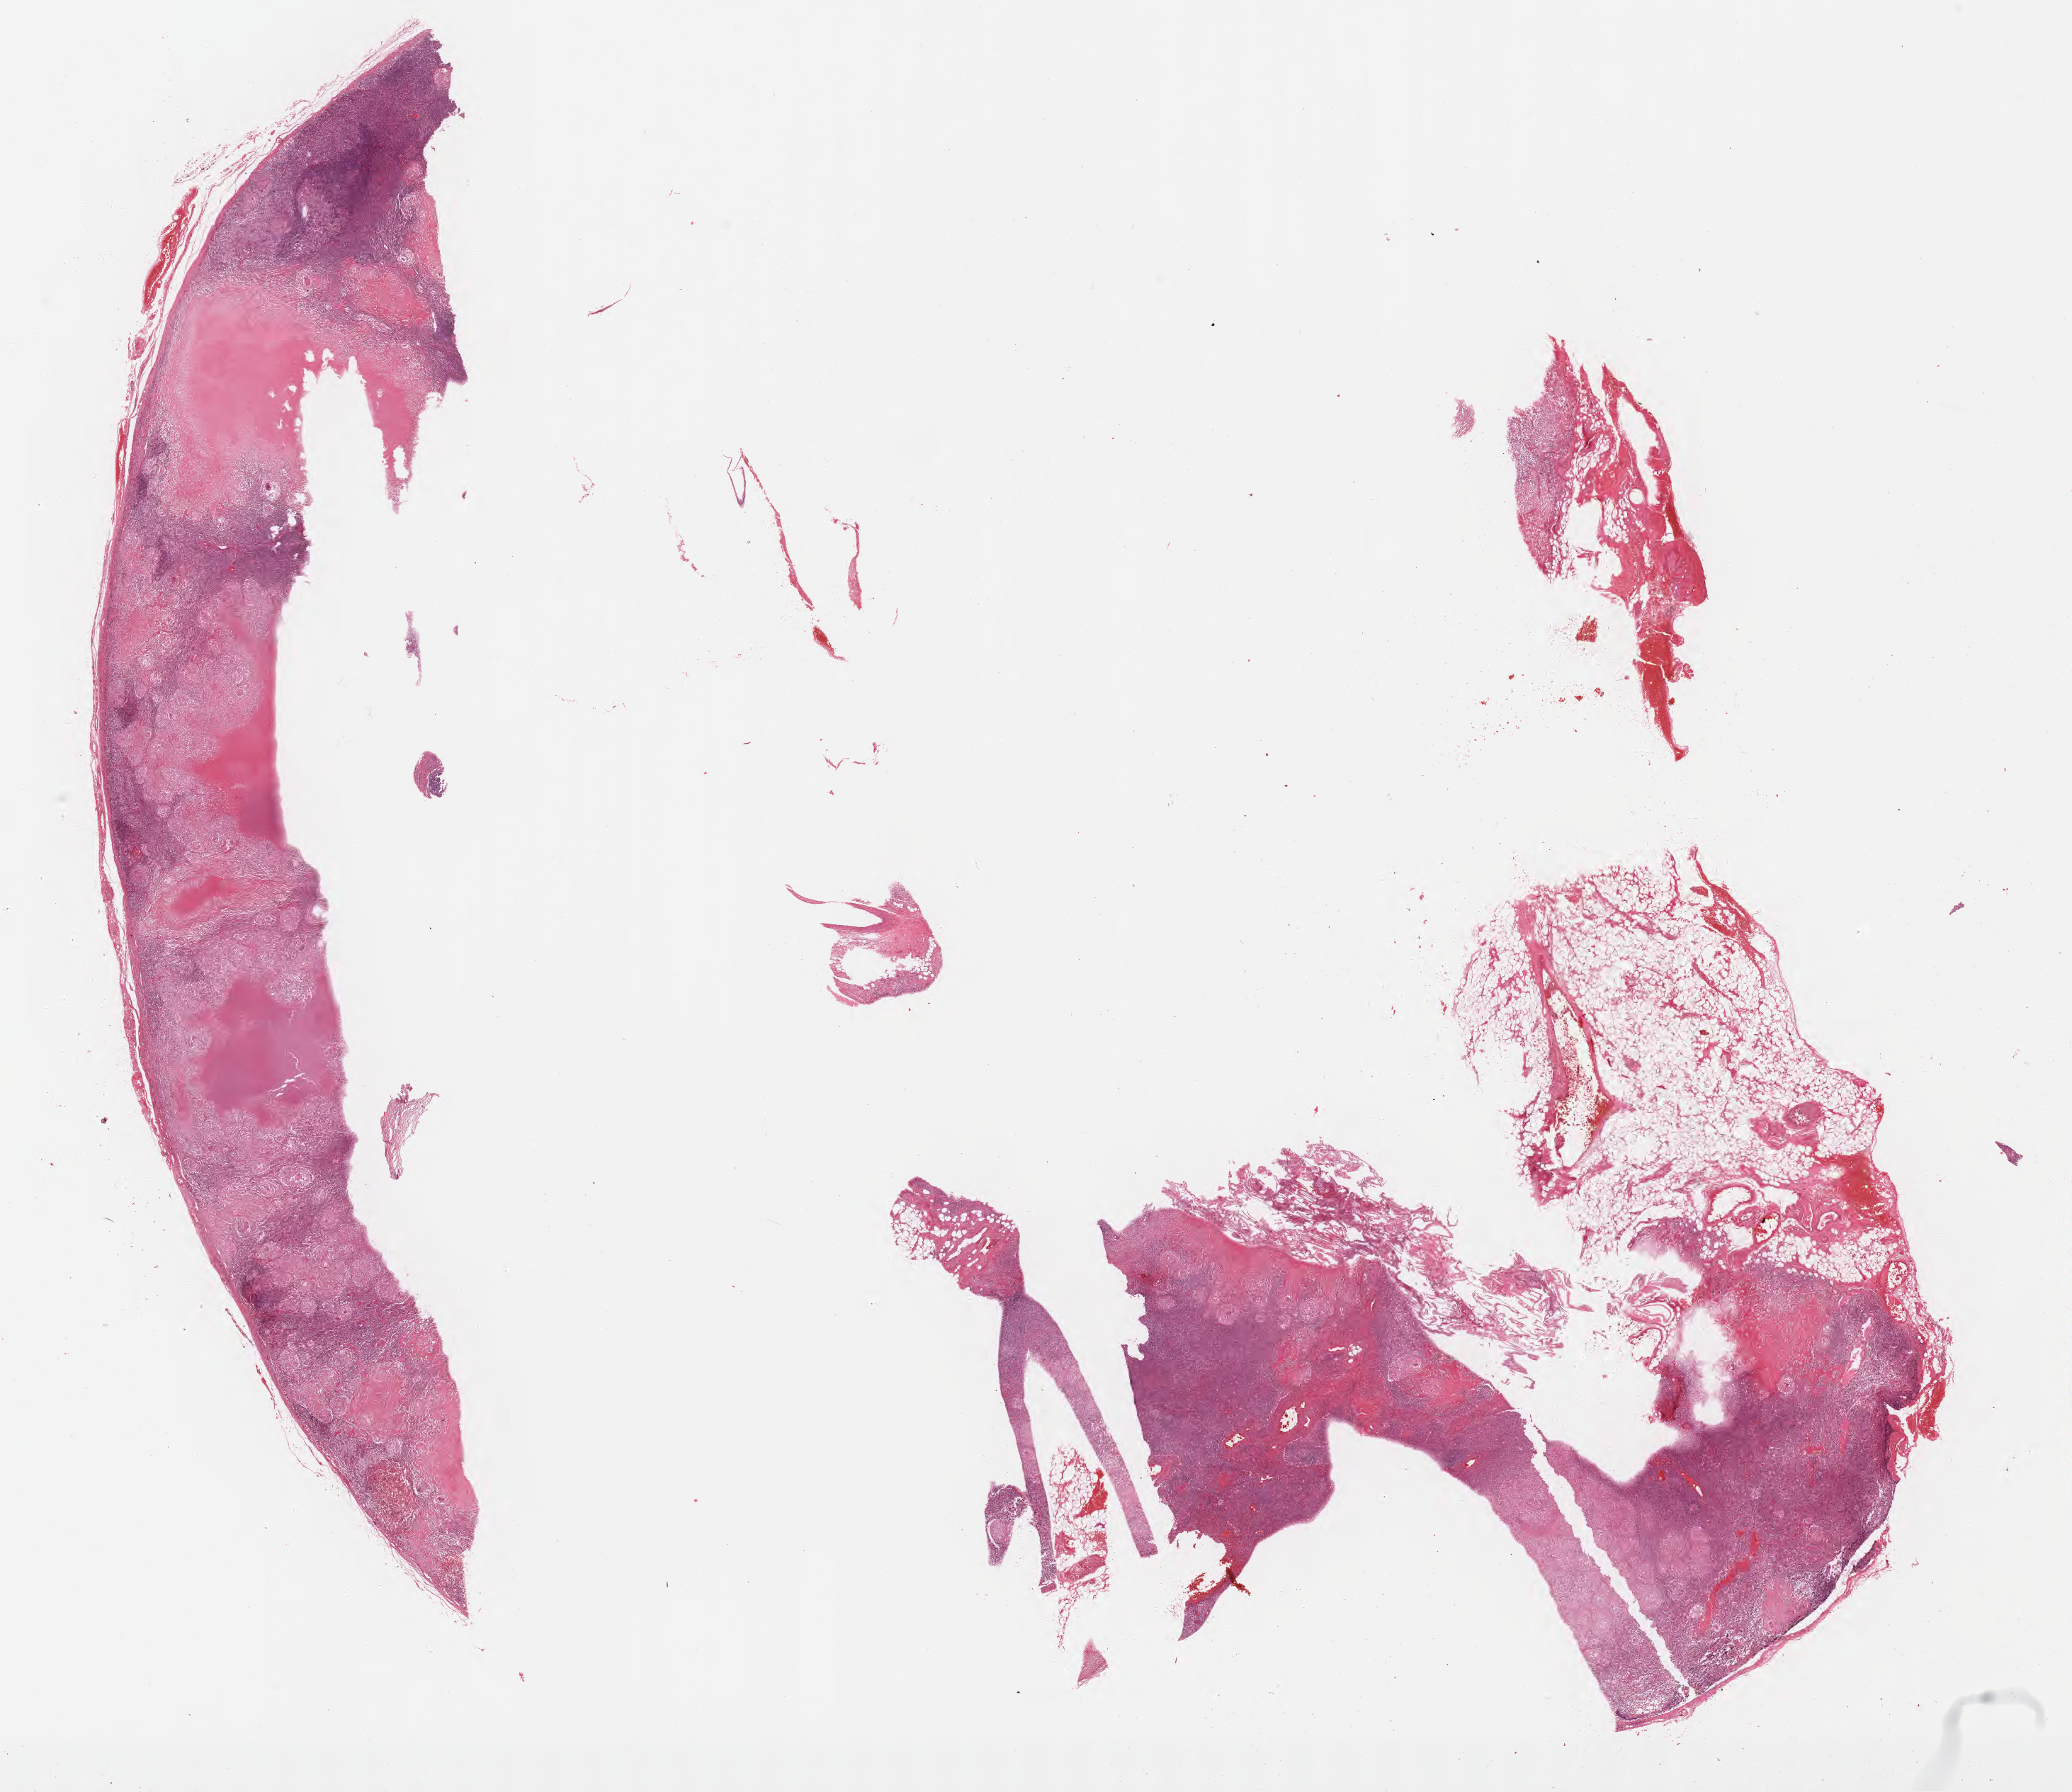
Digitized haematoxylin and eosin-stained section, a low-resolution overview of the entire scanned area, about 23.7 x 20.5 mm. FFPE section. Non-tumor (normal tissue) sample from a patient with burkitt lymphoma, NOS. Patient: male, aged 46. Slide review estimates, as recorded: tumor cells 0%, tumor nuclei 0%, stromal cells 20%, necrosis 40%, normal cells 40%. Infiltration values recorded for this section: lymphocyte infiltration 75%, monocyte infiltration 15%, neutrophil infiltration 5%.
This section: non-tumor tissue sample; the patient's diagnosis is given above.